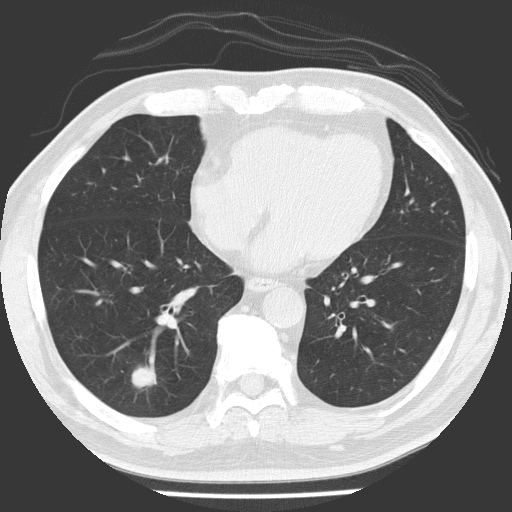
Low-dose screening chest CT, one axial slice; slice 61 of 154 in the series (ordered by position); reconstruction kernel FC51; lung window (W 1500 / L -600 HU); 2 mm slice thickness; 512 × 512 image matrix, field of view 311 × 311 mm.
Outlined on this slice (expert manual segmentation):
- lesion 1 (tumor, lower lobe of right lung): bounding box [x1, y1, x2, y2] px = [132, 366, 157, 388]